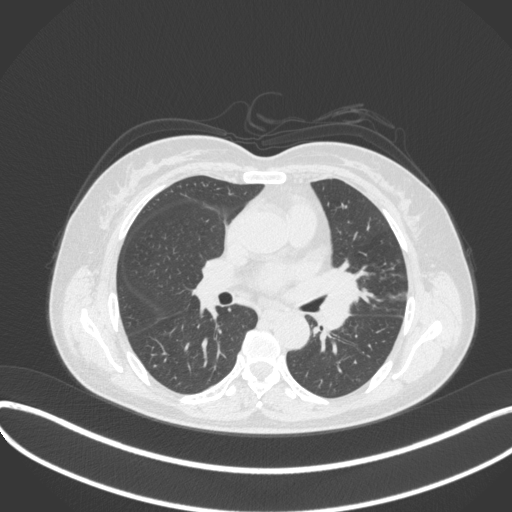
Chest CT, one axial slice. Position 192 of 373 along the scan axis. Lung window (W 1500 / L -600 HU). 512 × 512 image matrix, field of view 400 × 400 mm. Patient: female, 54 years. From the clinical record (not read from this slice): clinical TNM (as recorded): T2a N1 M0.
Outlined on this slice (rectangle marked by the reading radiologist):
- lung tumour (recorded histology: small cell carcinoma): bounding box <315,265,368,332> (left, top, right, bottom; pixels)